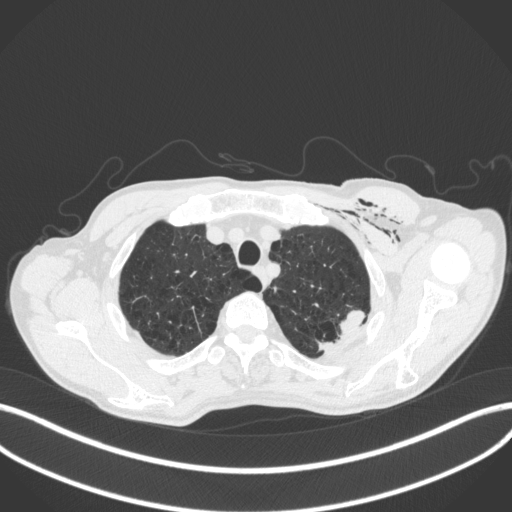
Chest CT, one axial slice. Slice 353 of 416 in the series (ordered by position). Lung window (W 1500 / L -600 HU). 1 mm slice thickness. 512 × 512 image matrix. Male patient, age 58 years. From the clinical record (not read from this slice): clinical TNM (as recorded): T3 N0 M0.
Structures marked on this image (bounding box drawn by a radiologist):
- lung tumour (recorded histology: adenocarcinoma): bounding box (x1, y1, x2, y2) in pixels: (305, 307, 367, 354)